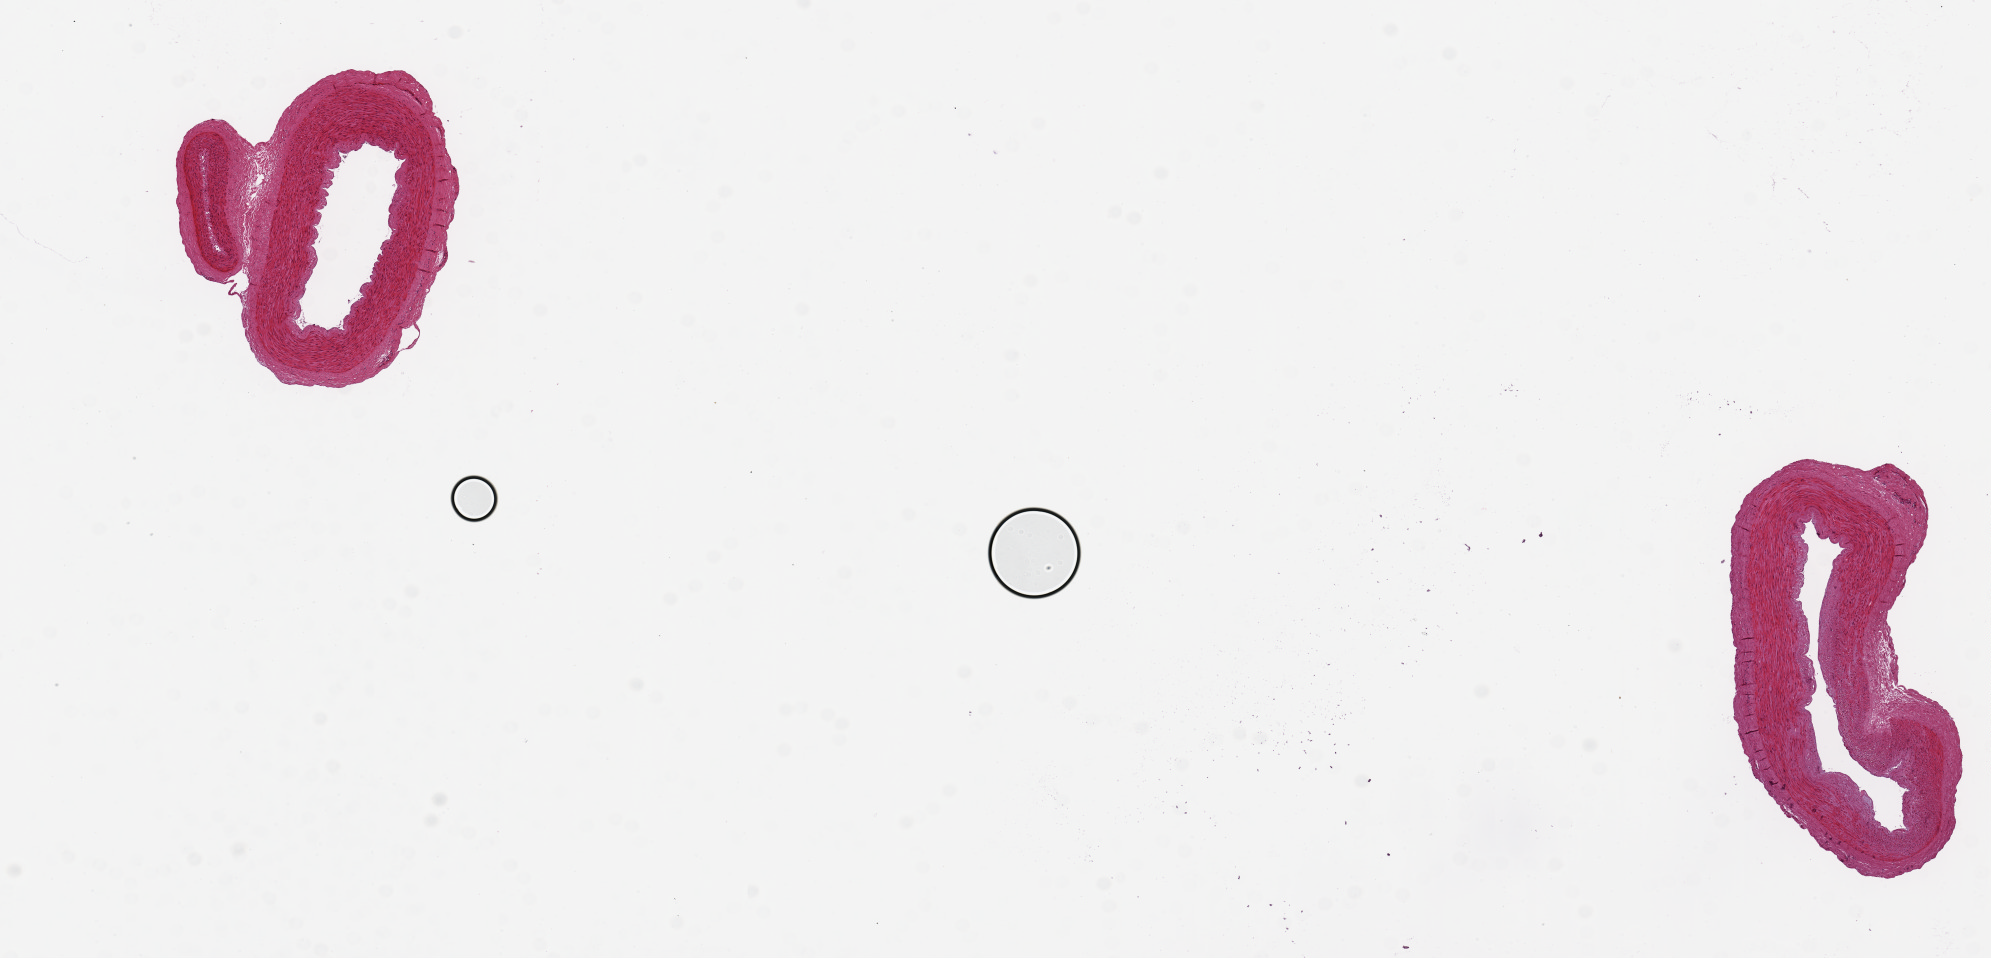
Whole-slide image, hematoxylin and eosin (H&E) stain, shown as a low-resolution overview of the whole scanned area (about 15.8 x 7.6 mm); PAXgene-fixed paraffin-embedded (PFPE) section; target tissue: tibial artery; donor tissue sample. Donor: male.
- review note (as recorded): 2 pieces, 3x1 & 3x2mm; ~2 mm clean arteries & 1 small branch; free of adipose